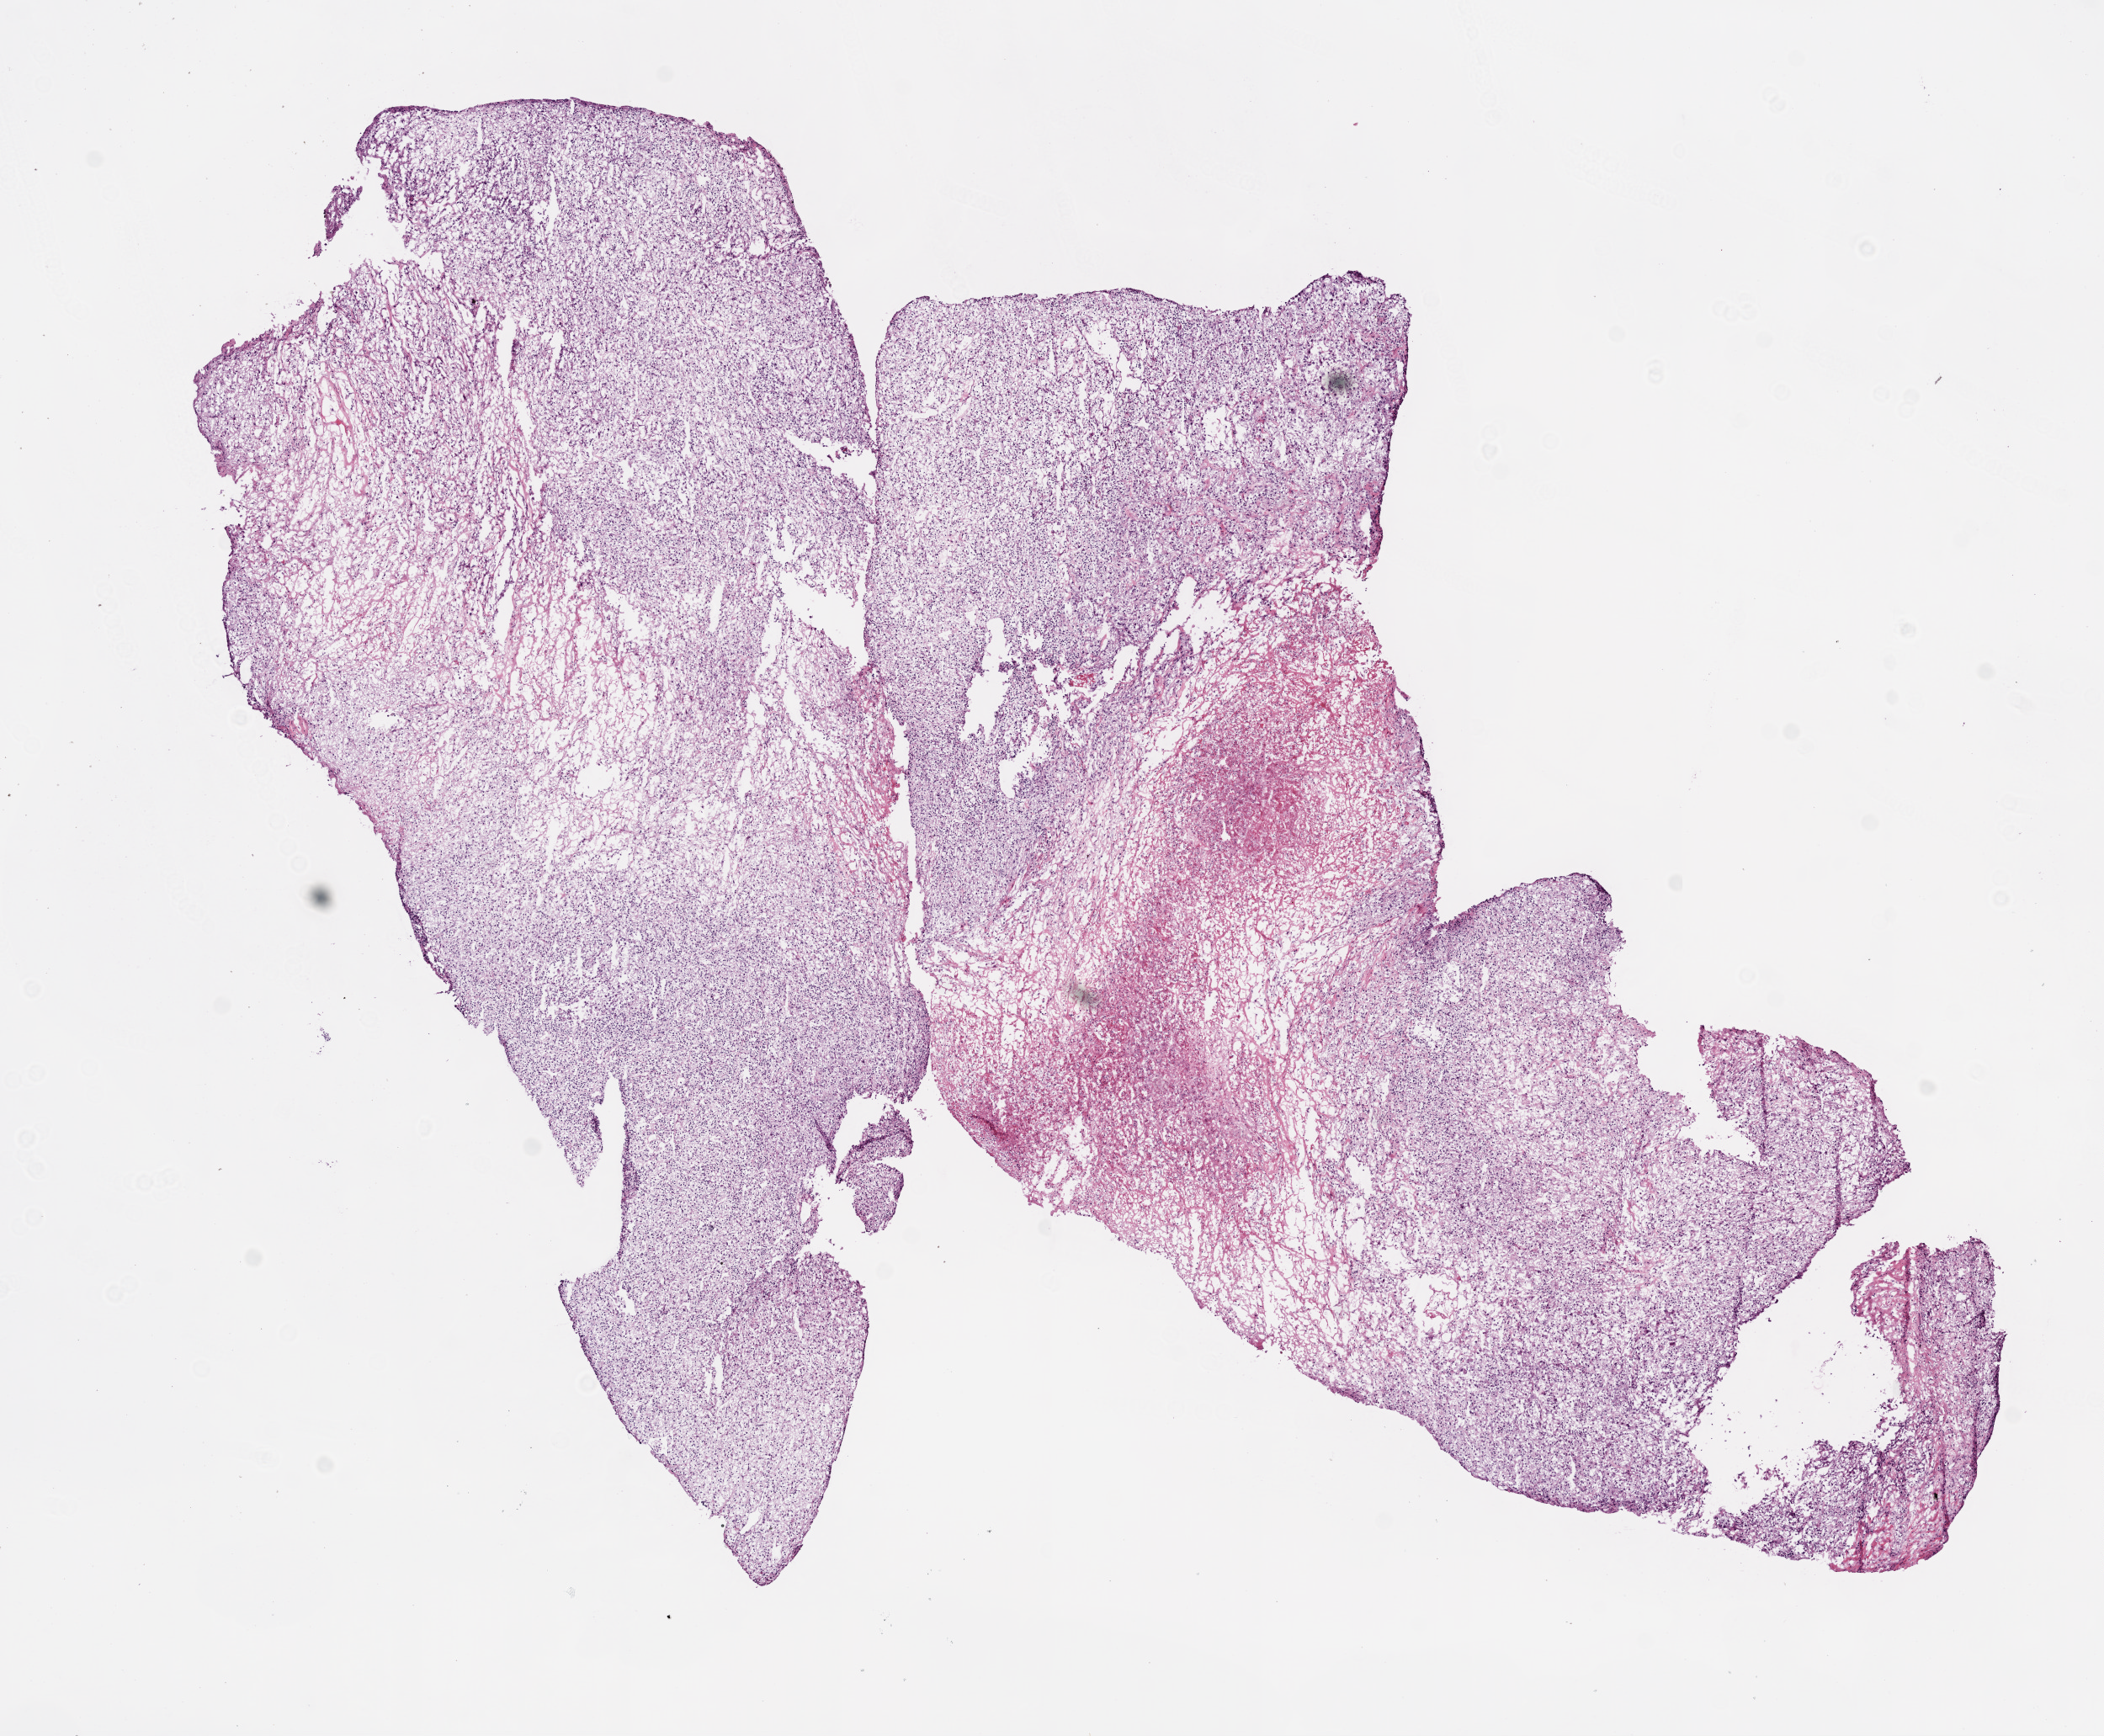
Whole-slide histology image, Hematoxylin and eosin (H&E) stained — whole scanned area (about 10.0 x 8.3 mm) shown as a low-resolution overview. Frozen section from the bottom of the tissue portion. Primary tumour sample from the kidney. Male patient; age at initial diagnosis 63 years. Histologic grade: G2 (moderately differentiated). Composition of this section per pathologist review: tumour cells 80%, tumour nuclei 85%, normal cells 0%, stromal cells 5%, necrosis 15%.
Histologic diagnosis: Clear cell adenocarcinoma, NOS. AJCC pathologic stage: II. TNM: T2 NX M0.